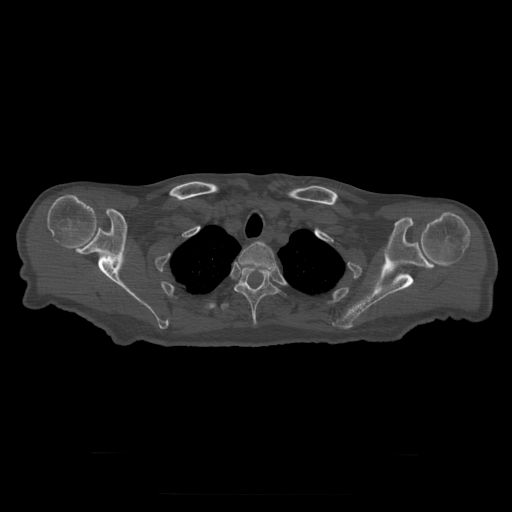
CT including the spine, one axial slice; slice 261 of 397 in the series (ordered by position); reconstruction kernel STANDARD; 120 kVp; bone window (W 1800 / L 400 HU); 1.25 mm slice thickness; 512 × 512 image matrix, field of view 510 × 510 mm. Patient age 73 years. Case-level facts recorded for this patient, not image findings: primary cancer: prostate.
Structures marked on this image (semi-automatically segmented with operator editing):
- T2 vertebra: bounding box [x1, y1, x2, y2] px = [238, 242, 276, 271]
- T3 vertebra: [235, 267, 280, 325]
- T4 vertebra: [221, 303, 230, 311]